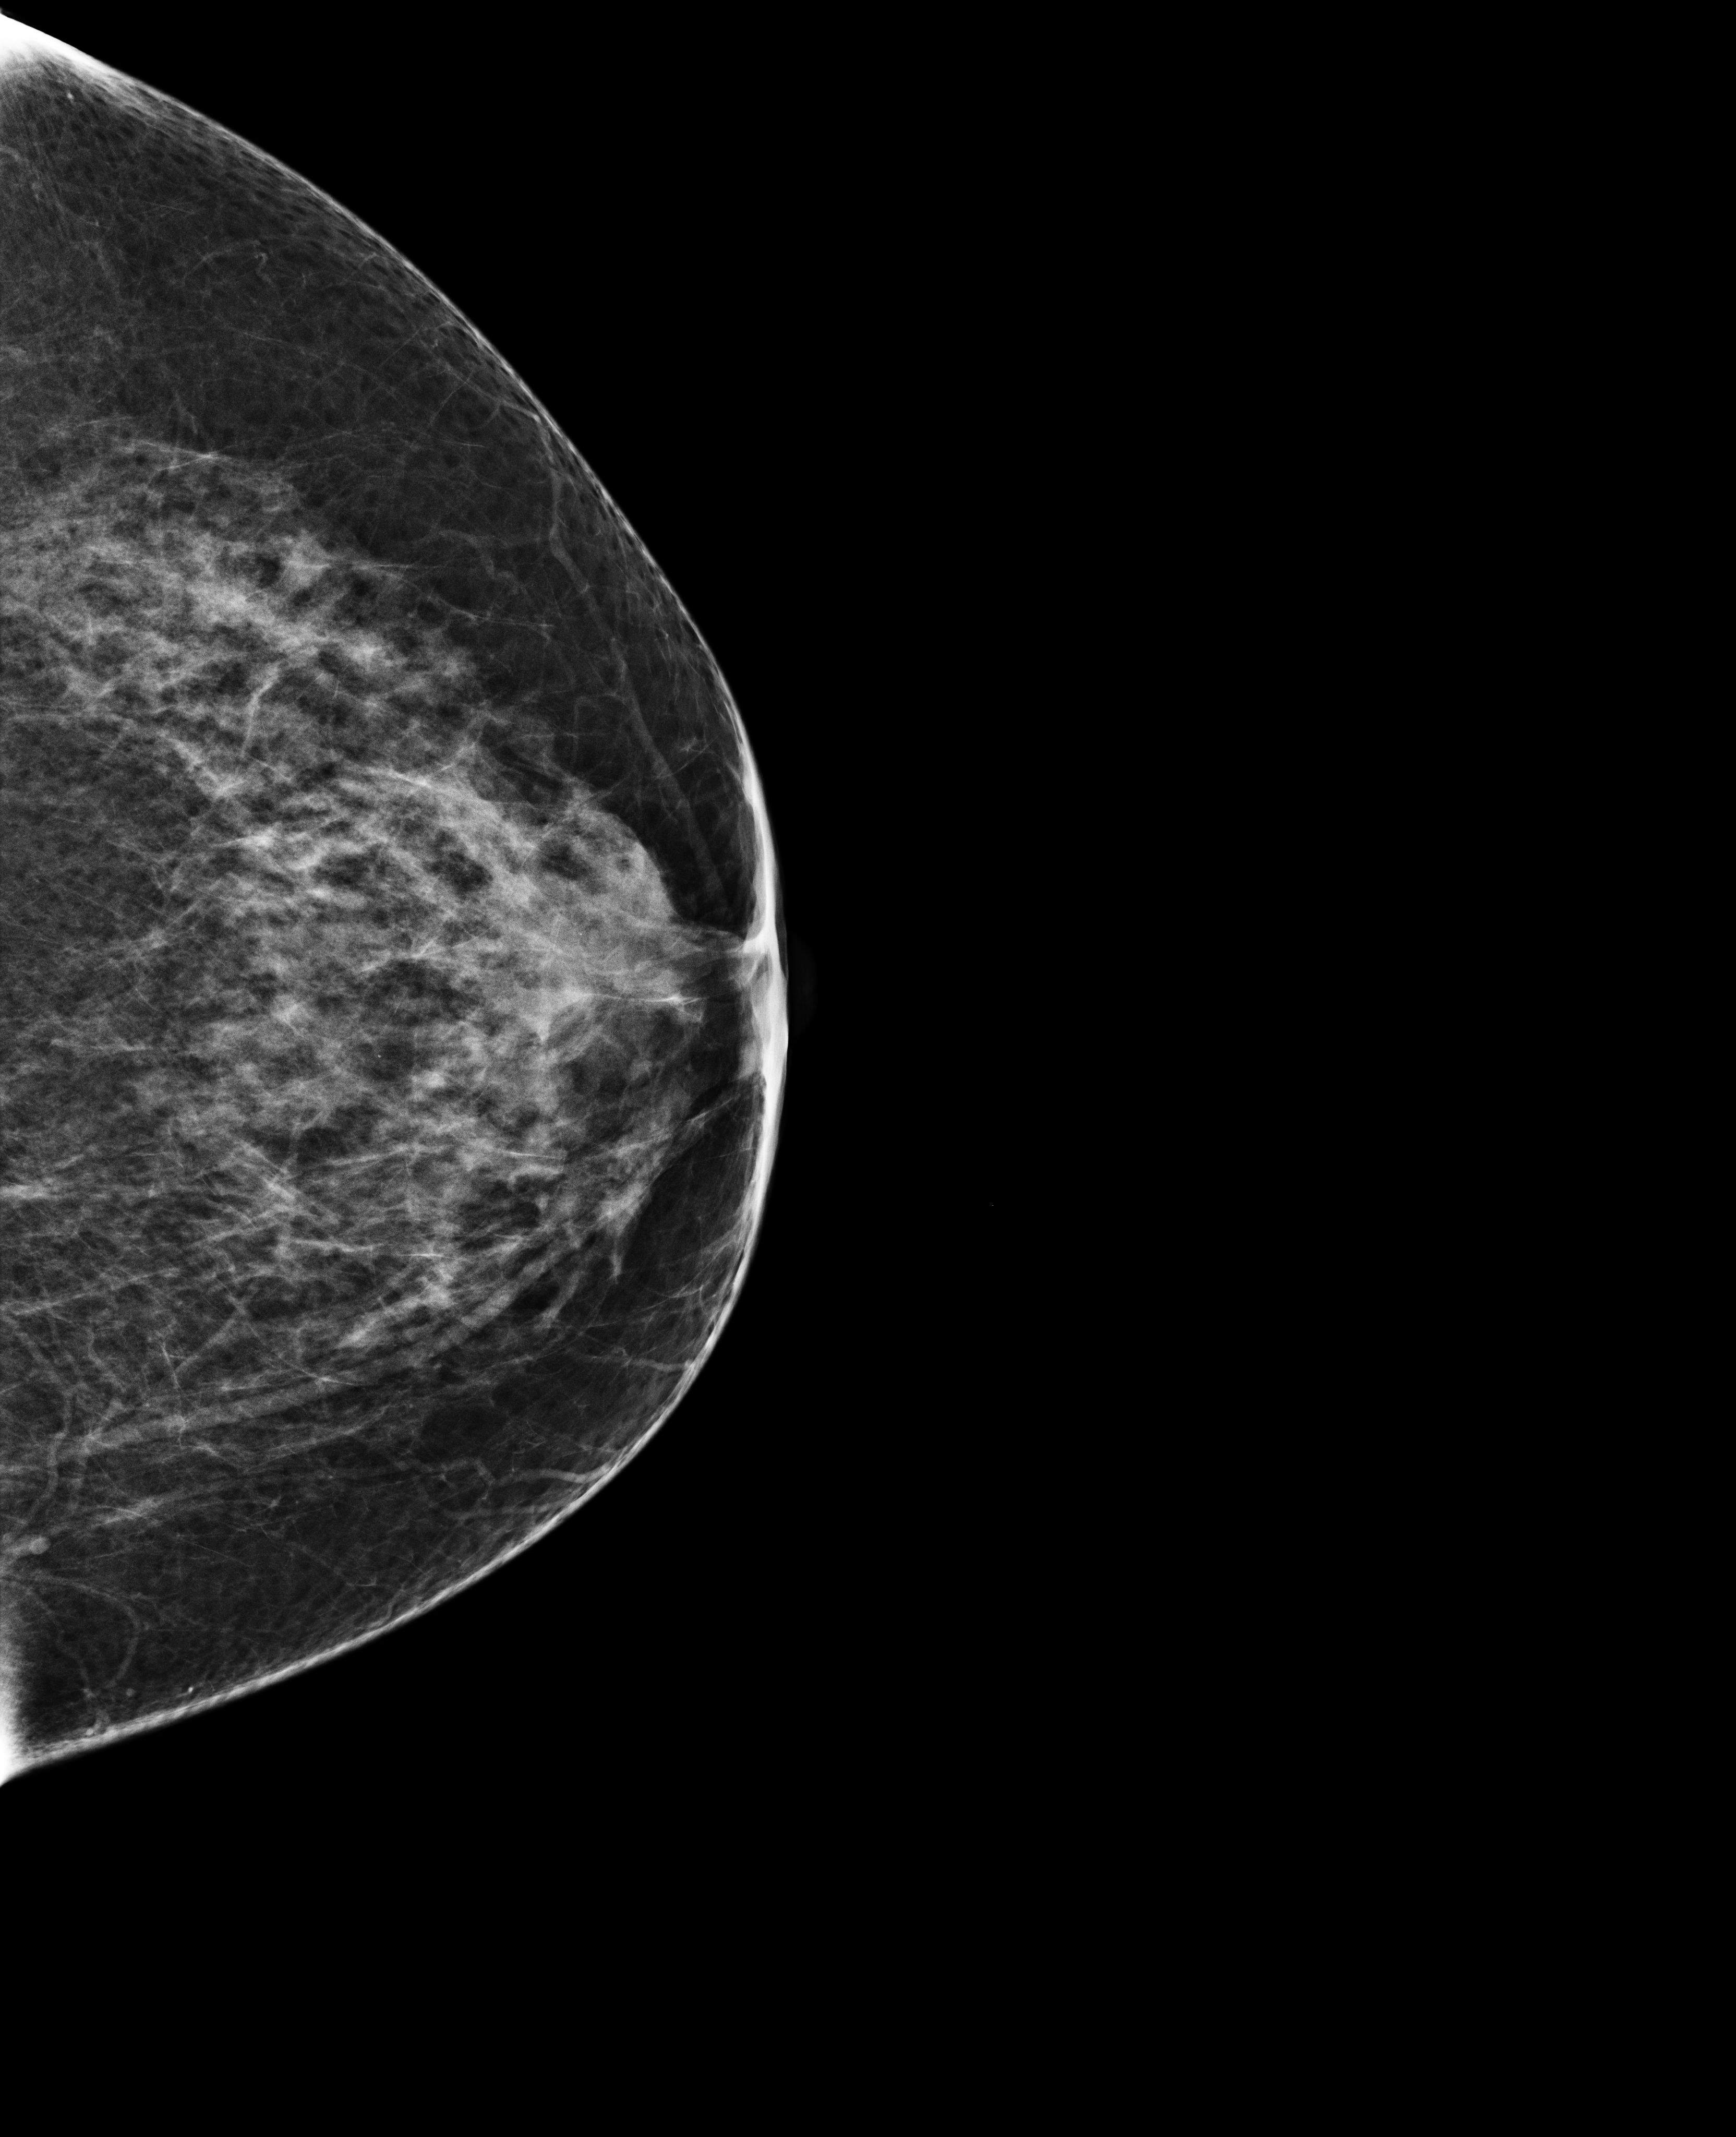
Digital mammogram (FFDM); left breast; cranio-caudal projection; annual screening mammography examination; compressed breast thickness 58 mm; system: Selenia Dimensions. Patient aged 71 years (female).
Final BI-RADS category for the screening round (tomosynthesis exam, both breasts): category 2.